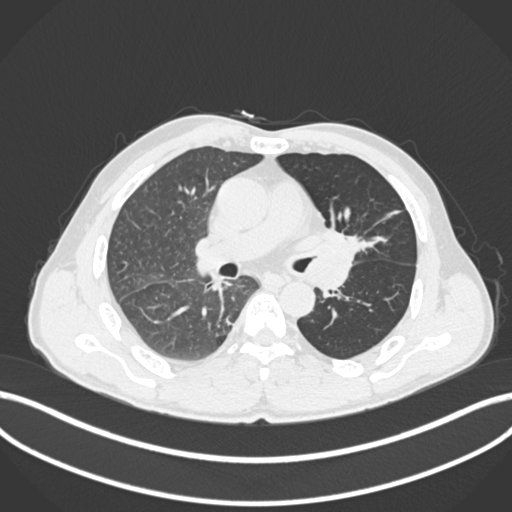
Chest CT, one axial slice. 120 kVp. Lung window (W 1500 / L -600 HU). 1 mm slice thickness. 512 × 512 image matrix, field of view 400 × 400 mm. Patient: male, 57 years. From the clinical record (not read from this slice): clinical TNM (as recorded): T2b N0 M0.
Outlined on this slice (bounding box drawn by a radiologist):
- lung tumour (recorded histology: squamous cell carcinoma): bounding box [x1, y1, x2, y2] px = [320, 225, 378, 270]